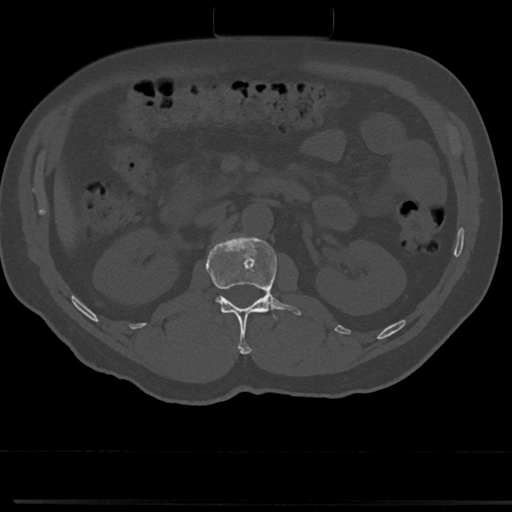
CT including the spine, one axial slice; position 71 of 817 along the scan axis; 120 kVp; bone window (W 1800 / L 400 HU); 0.5 mm slice thickness; 512 × 512 image matrix. Male patient, age 61 years. Case-level facts recorded for this patient, not image findings: primary cancer: prostate.
Annotated regions visible in this slice (semi-automatically segmented with operator editing):
- L1 vertebra: bounding box [x1, y1, x2, y2] px = [208, 235, 302, 354]